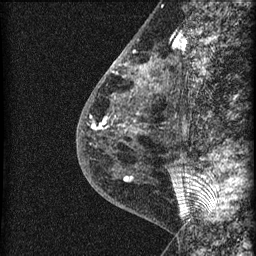
Breast MRI (dynamic contrast-enhanced), one sagittal slice. Slice 23 of 60 in the series (ordered by position). Dynamic contrast-enhanced series, image 2 of 3 at this slice position (ordered by acquisition). 1.5 T. TE 4.2 ms, TR 22.7 ms. 256 × 256 image matrix, field of view 180 × 180 mm. Female patient, age 48 years. Case-level facts recorded for this patient, not image findings: setting: breast cancer imaged before/during neoadjuvant chemotherapy; receptor status: triple-negative.
Annotated regions visible in this slice (semi-automatic segmentation, software-assisted and operator-edited):
- analysis volume of interest (the breast-tissue region the enhancement analysis was run in; not a lesion): box from (x=115, y=34) to (x=169, y=162) px
- tumour enhancement mask (voxels above the 90 % enhancement threshold inside the analysis volume of interest): (x=140, y=63)–(x=152, y=73)